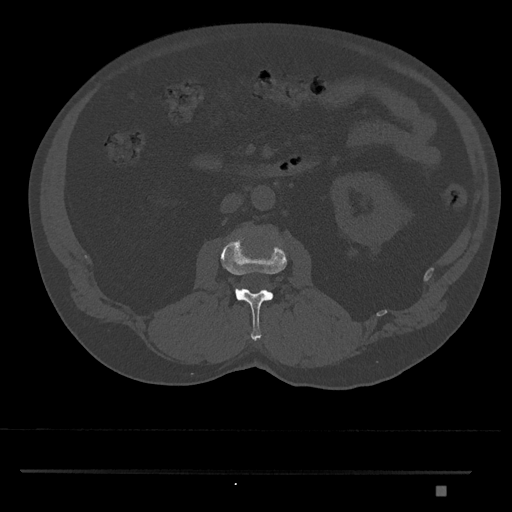
CT including the spine, one axial slice. Slice 737 of 1134 in the series (ordered by position). Bone window (W 1800 / L 400 HU). 0.5 mm slice thickness. 512 × 512 image matrix, field of view 429 × 429 mm. Patient: male, 65 years. From the clinical record (not read from this slice): primary cancer: prostate.
Outlined on this slice (semi-automatically segmented with operator editing):
- L2 vertebra: bounding box <220,237,287,341> (left, top, right, bottom; pixels)